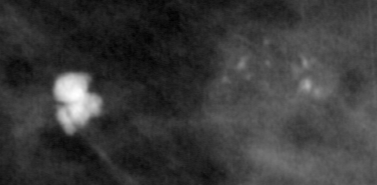
Crop from a digitized film mammogram around one marked abnormality, right breast, CC view, BI-RADS breast density category 3 (scale 1–4).
Finding: calcifications, morphology pleomorphic, distribution clustered; BI-RADS assessment category 4; subtlety rating 2 on a 1 (subtle) to 5 (obvious) scale; pathology (as recorded): benign.